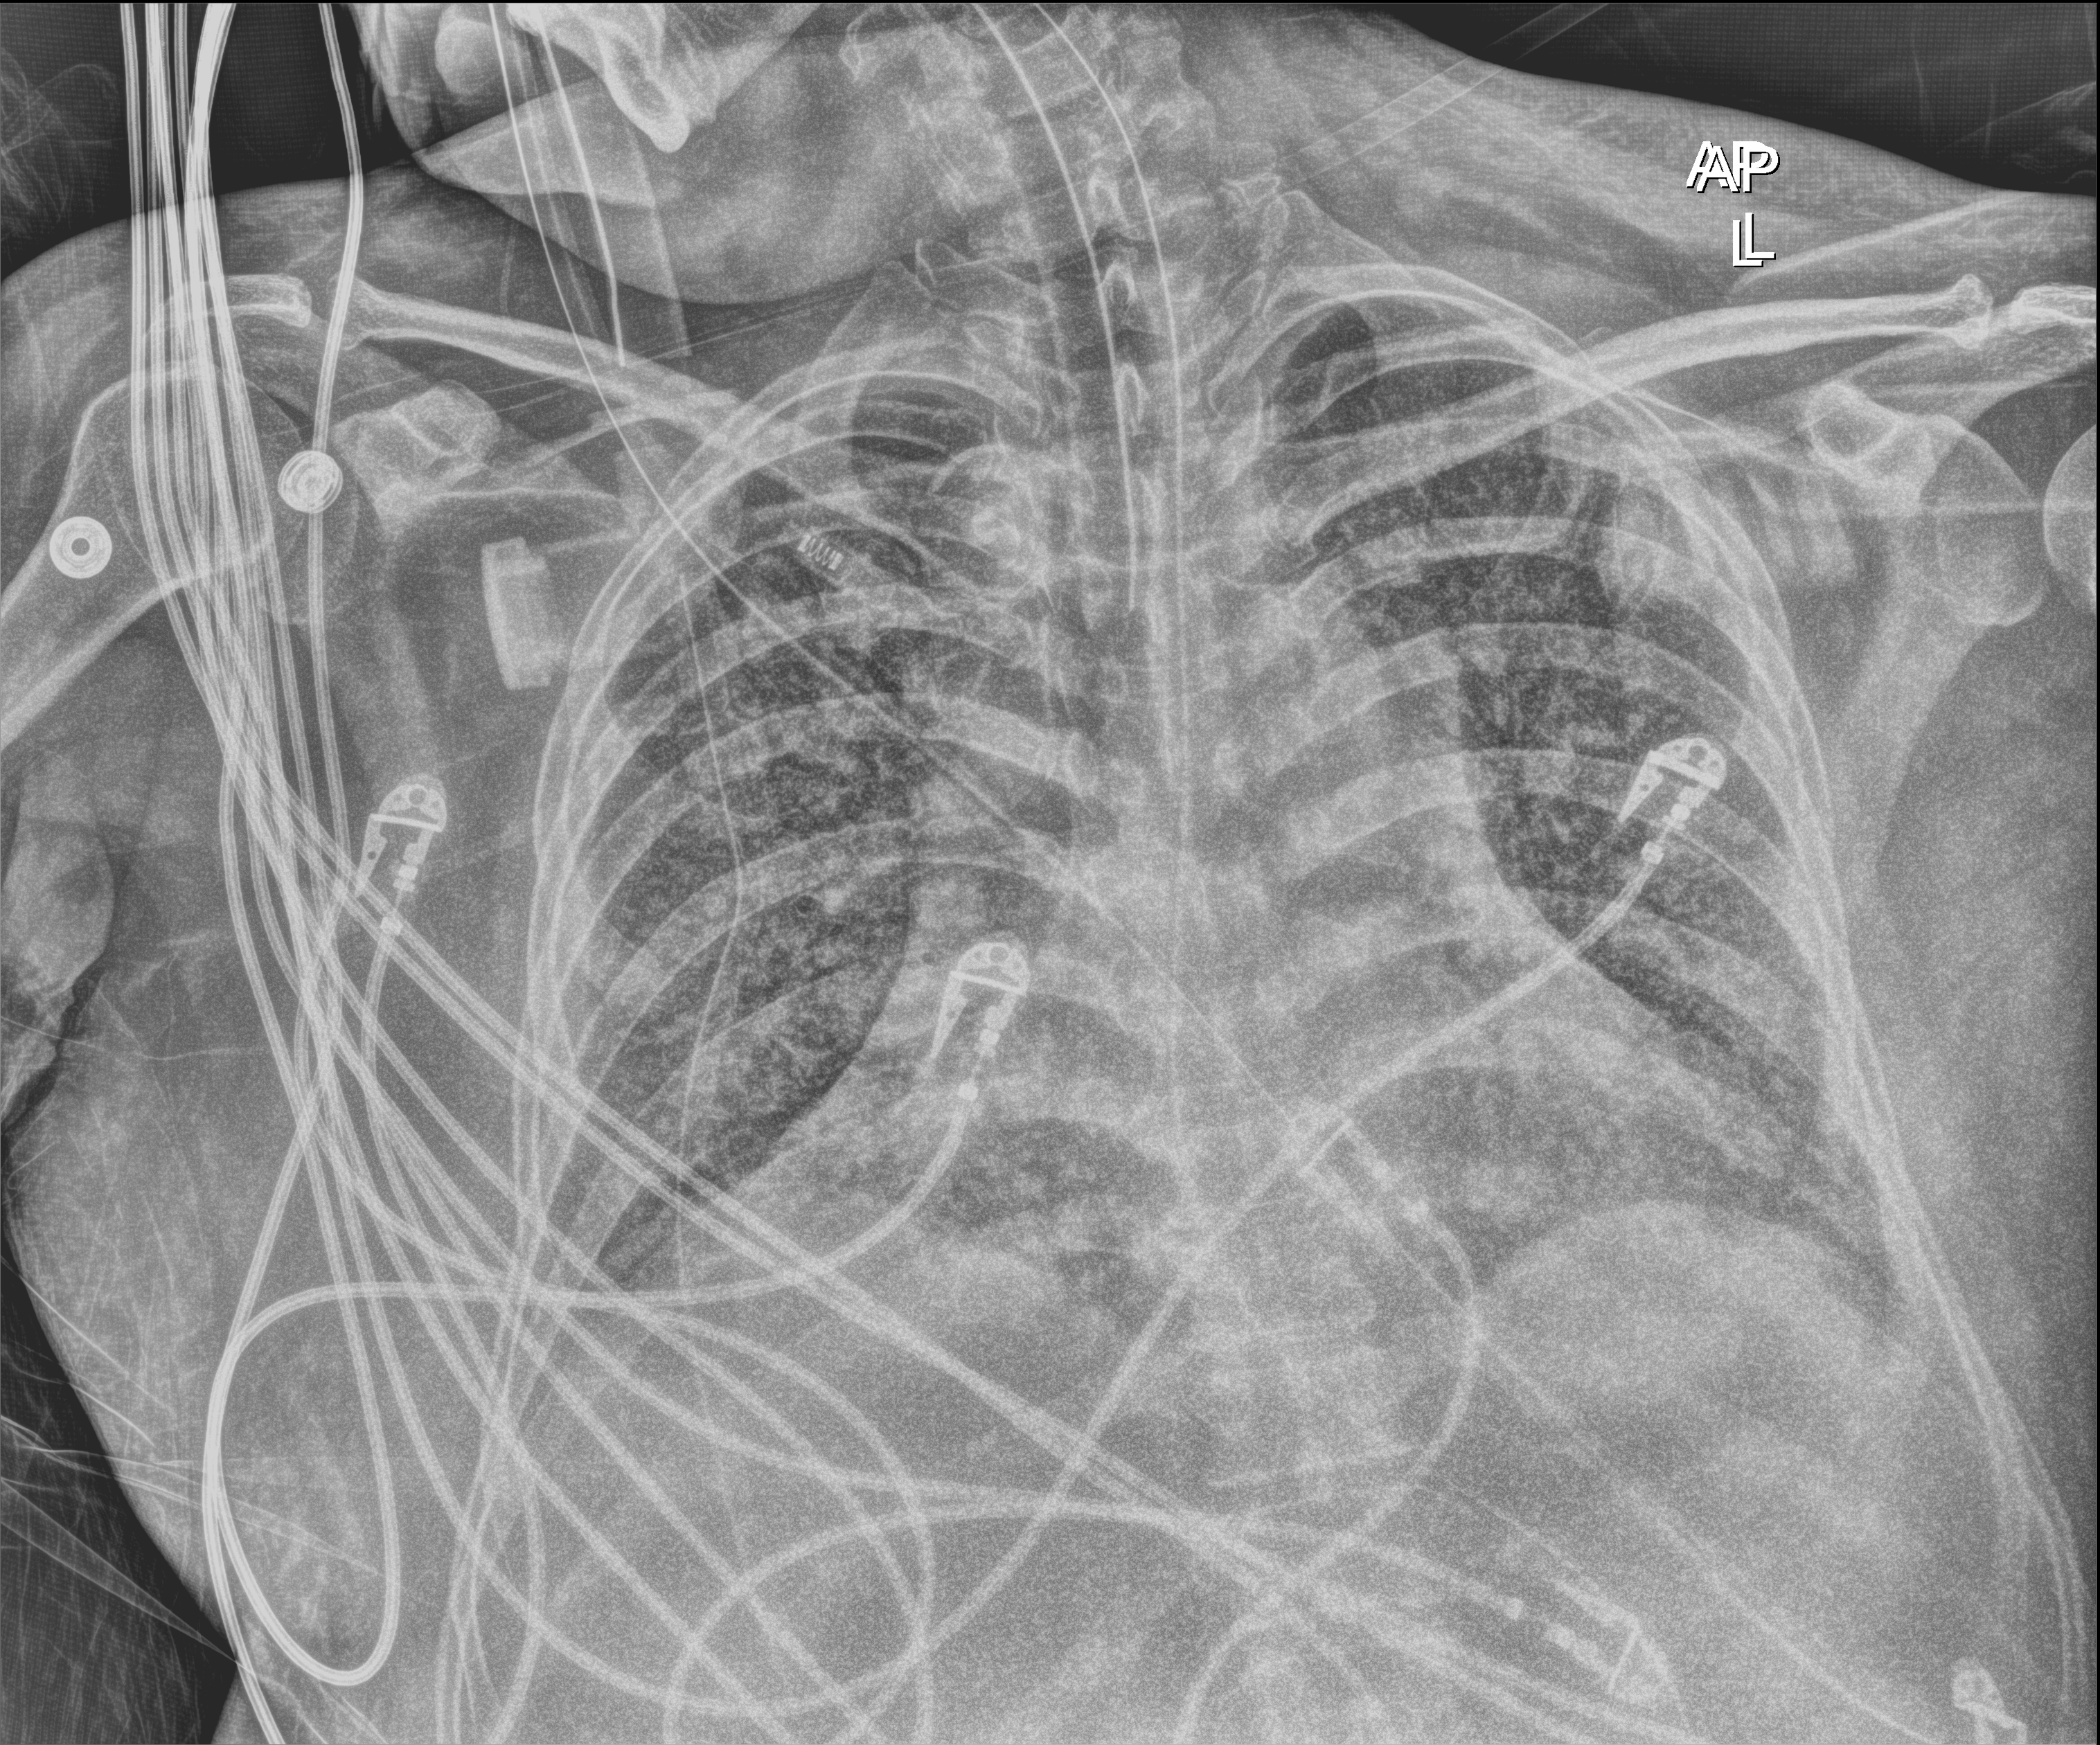
Chest X-ray (portable); anteroposterior (AP) projection. Adult patient hospitalised with COVID-19, age 18–59 years.
Admission-level facts for this patient (not findings on this image; timing relative to this image not recorded):
- admitted to intensive care during this hospital stay: yes
- length of hospital stay: 48 days